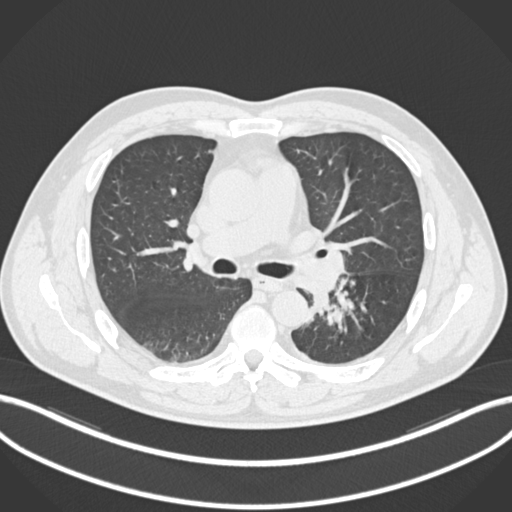
Chest CT, one axial slice; position 136 of 223 along the scan axis; 120 kVp; lung window (W 1500 / L -600 HU); 1 mm slice thickness; 512 × 512 image matrix. Male patient, age 50 years. Case-level facts recorded for this patient, not image findings: clinical TNM (as recorded): T2a N3 M0.
Outlined on this slice (rectangle marked by the reading radiologist):
- lung tumour (recorded histology: squamous cell carcinoma): bounding box <311,281,353,328> (left, top, right, bottom; pixels)